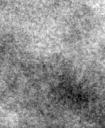
Cropped region of a digitized screen-film mammogram centred on a radiologist-marked abnormality, right breast, MLO view, BI-RADS breast density category 2 (scale 1–4).
Marked abnormality: calcifications, morphology pleomorphic / fine linear branching, distribution segmental; BI-RADS assessment category 5; subtlety rating 5 on a 1 (subtle) to 5 (obvious) scale; pathology (as recorded): malignant.